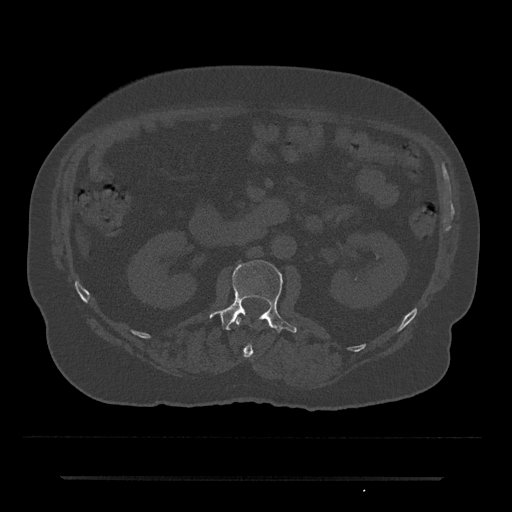
CT including the spine, one axial slice; slice 24 of 797 in the series (ordered by position); reconstruction kernel Br40s/3; 120 kVp; bone window (W 1800 / L 400 HU); 0.5 mm slice thickness; 512 × 512 image matrix. Patient: male, 69 years. Case-level facts recorded for this patient, not image findings: primary cancer: prostate.
Structures marked on this image (semi-automatically segmented with operator editing):
- L1 vertebra: bounding box <235,316,266,358> (left, top, right, bottom; pixels)
- L2 vertebra: <210,260,297,333>